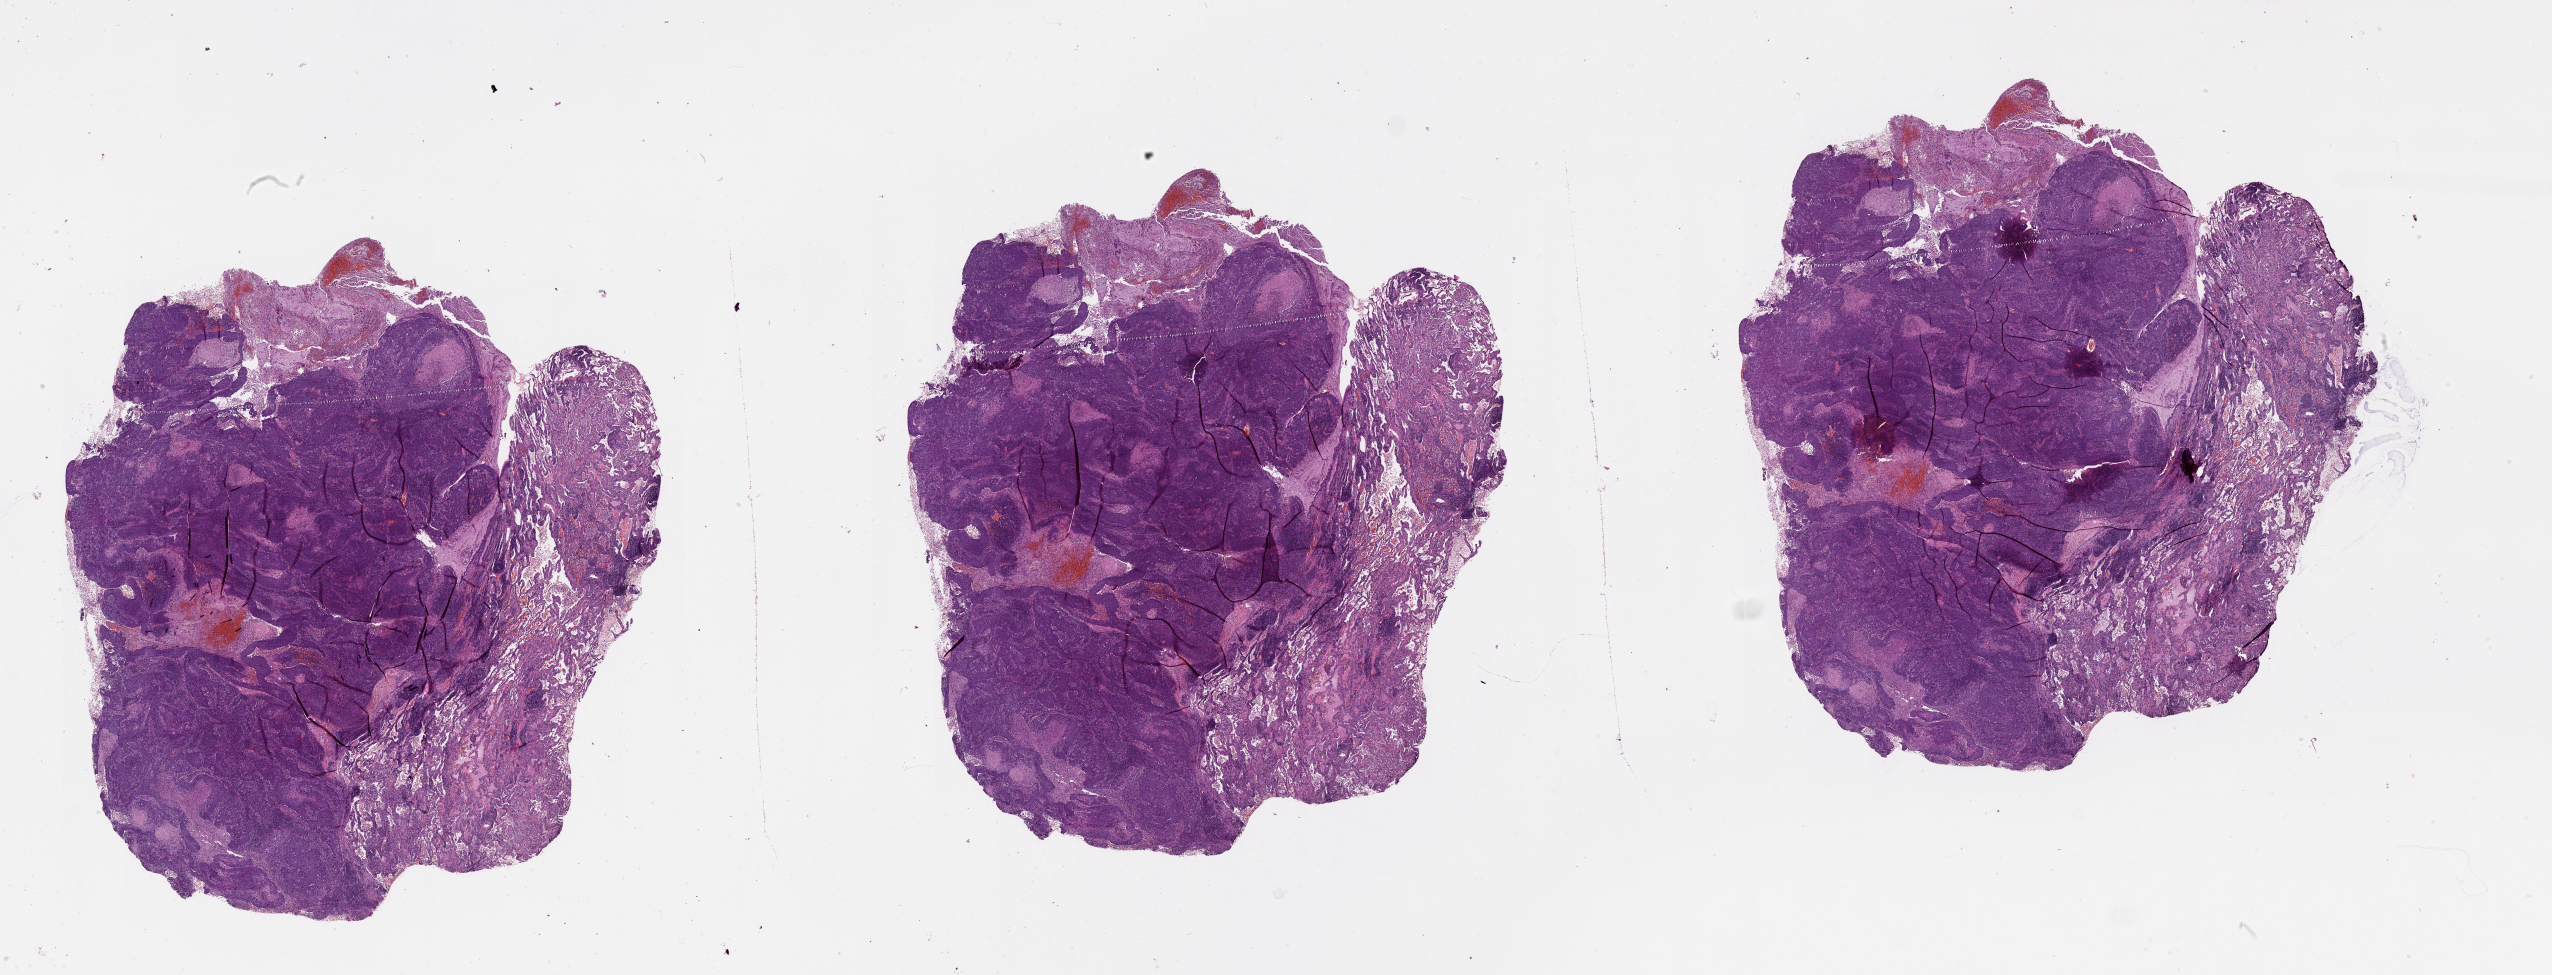
Whole-slide histology image, Hematoxylin and eosin (H&E) stained — shown as a low-resolution overview of the whole scanned area (about 41.1 x 15.7 mm); lung, tumour tissue. Male, 53 y/o.
Patient diagnosis (cohort enrolment): squamous cell carcinoma (lung).